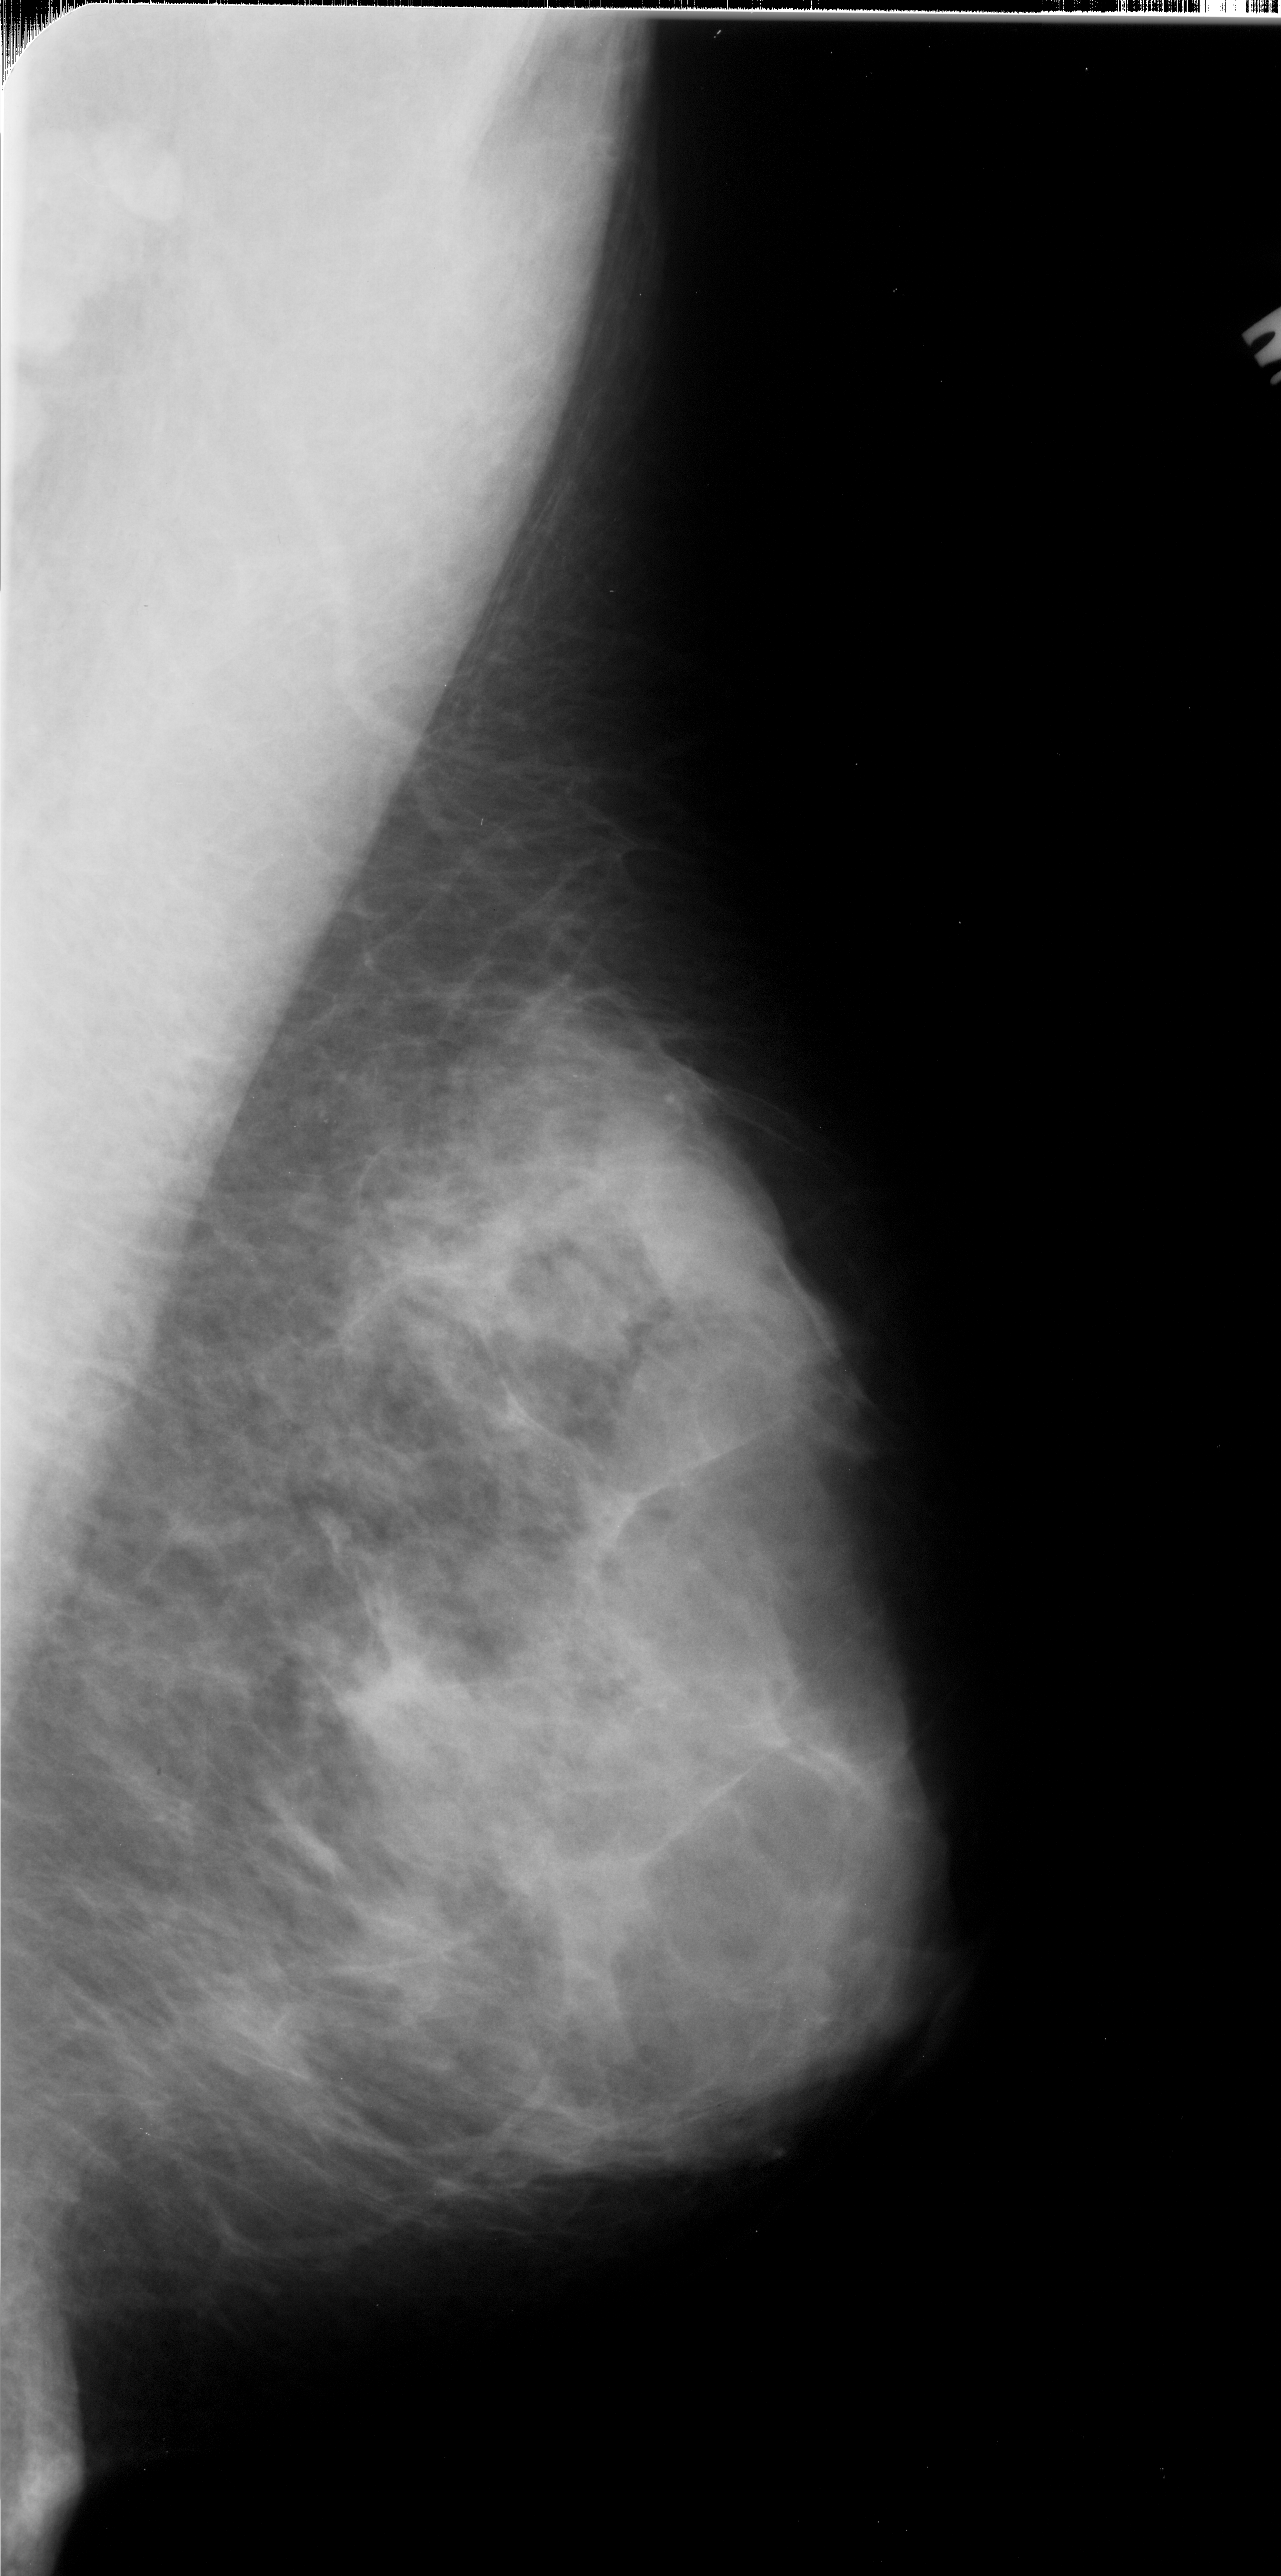
Scanned film-screen mammogram; right breast; MLO view; 1281 × 2576 image matrix.
Expert-marked regions of interest on this film, with their recorded descriptors:
- calcifications, morphology pleomorphic, distribution clustered; BI-RADS assessment category 4; subtlety rating 1 on a 1 (subtle) to 5 (obvious) scale; pathology (as recorded): malignant: bounding box <515,1418,616,1507> (left, top, right, bottom; pixels)